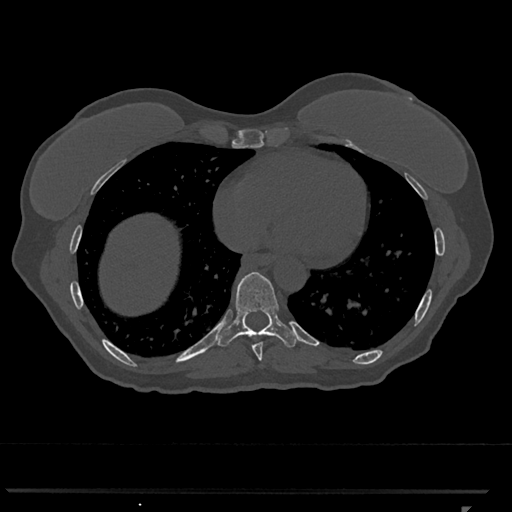
CT including the spine, one axial slice; slice 630 of 793 in the series (ordered by position); 120 kVp; bone window (W 1800 / L 400 HU); 0.5 mm slice thickness; 512 × 512 image matrix, field of view 380 × 380 mm. Patient: female, 62 years. Case-level facts recorded for this patient, not image findings: primary cancer: renal.
Annotated regions visible in this slice (semi-automatic segmentation, software-assisted and operator-edited):
- T8 vertebra: box from (x=252, y=343) to (x=263, y=361) px
- T9 vertebra: (x=216, y=272)–(x=298, y=348)